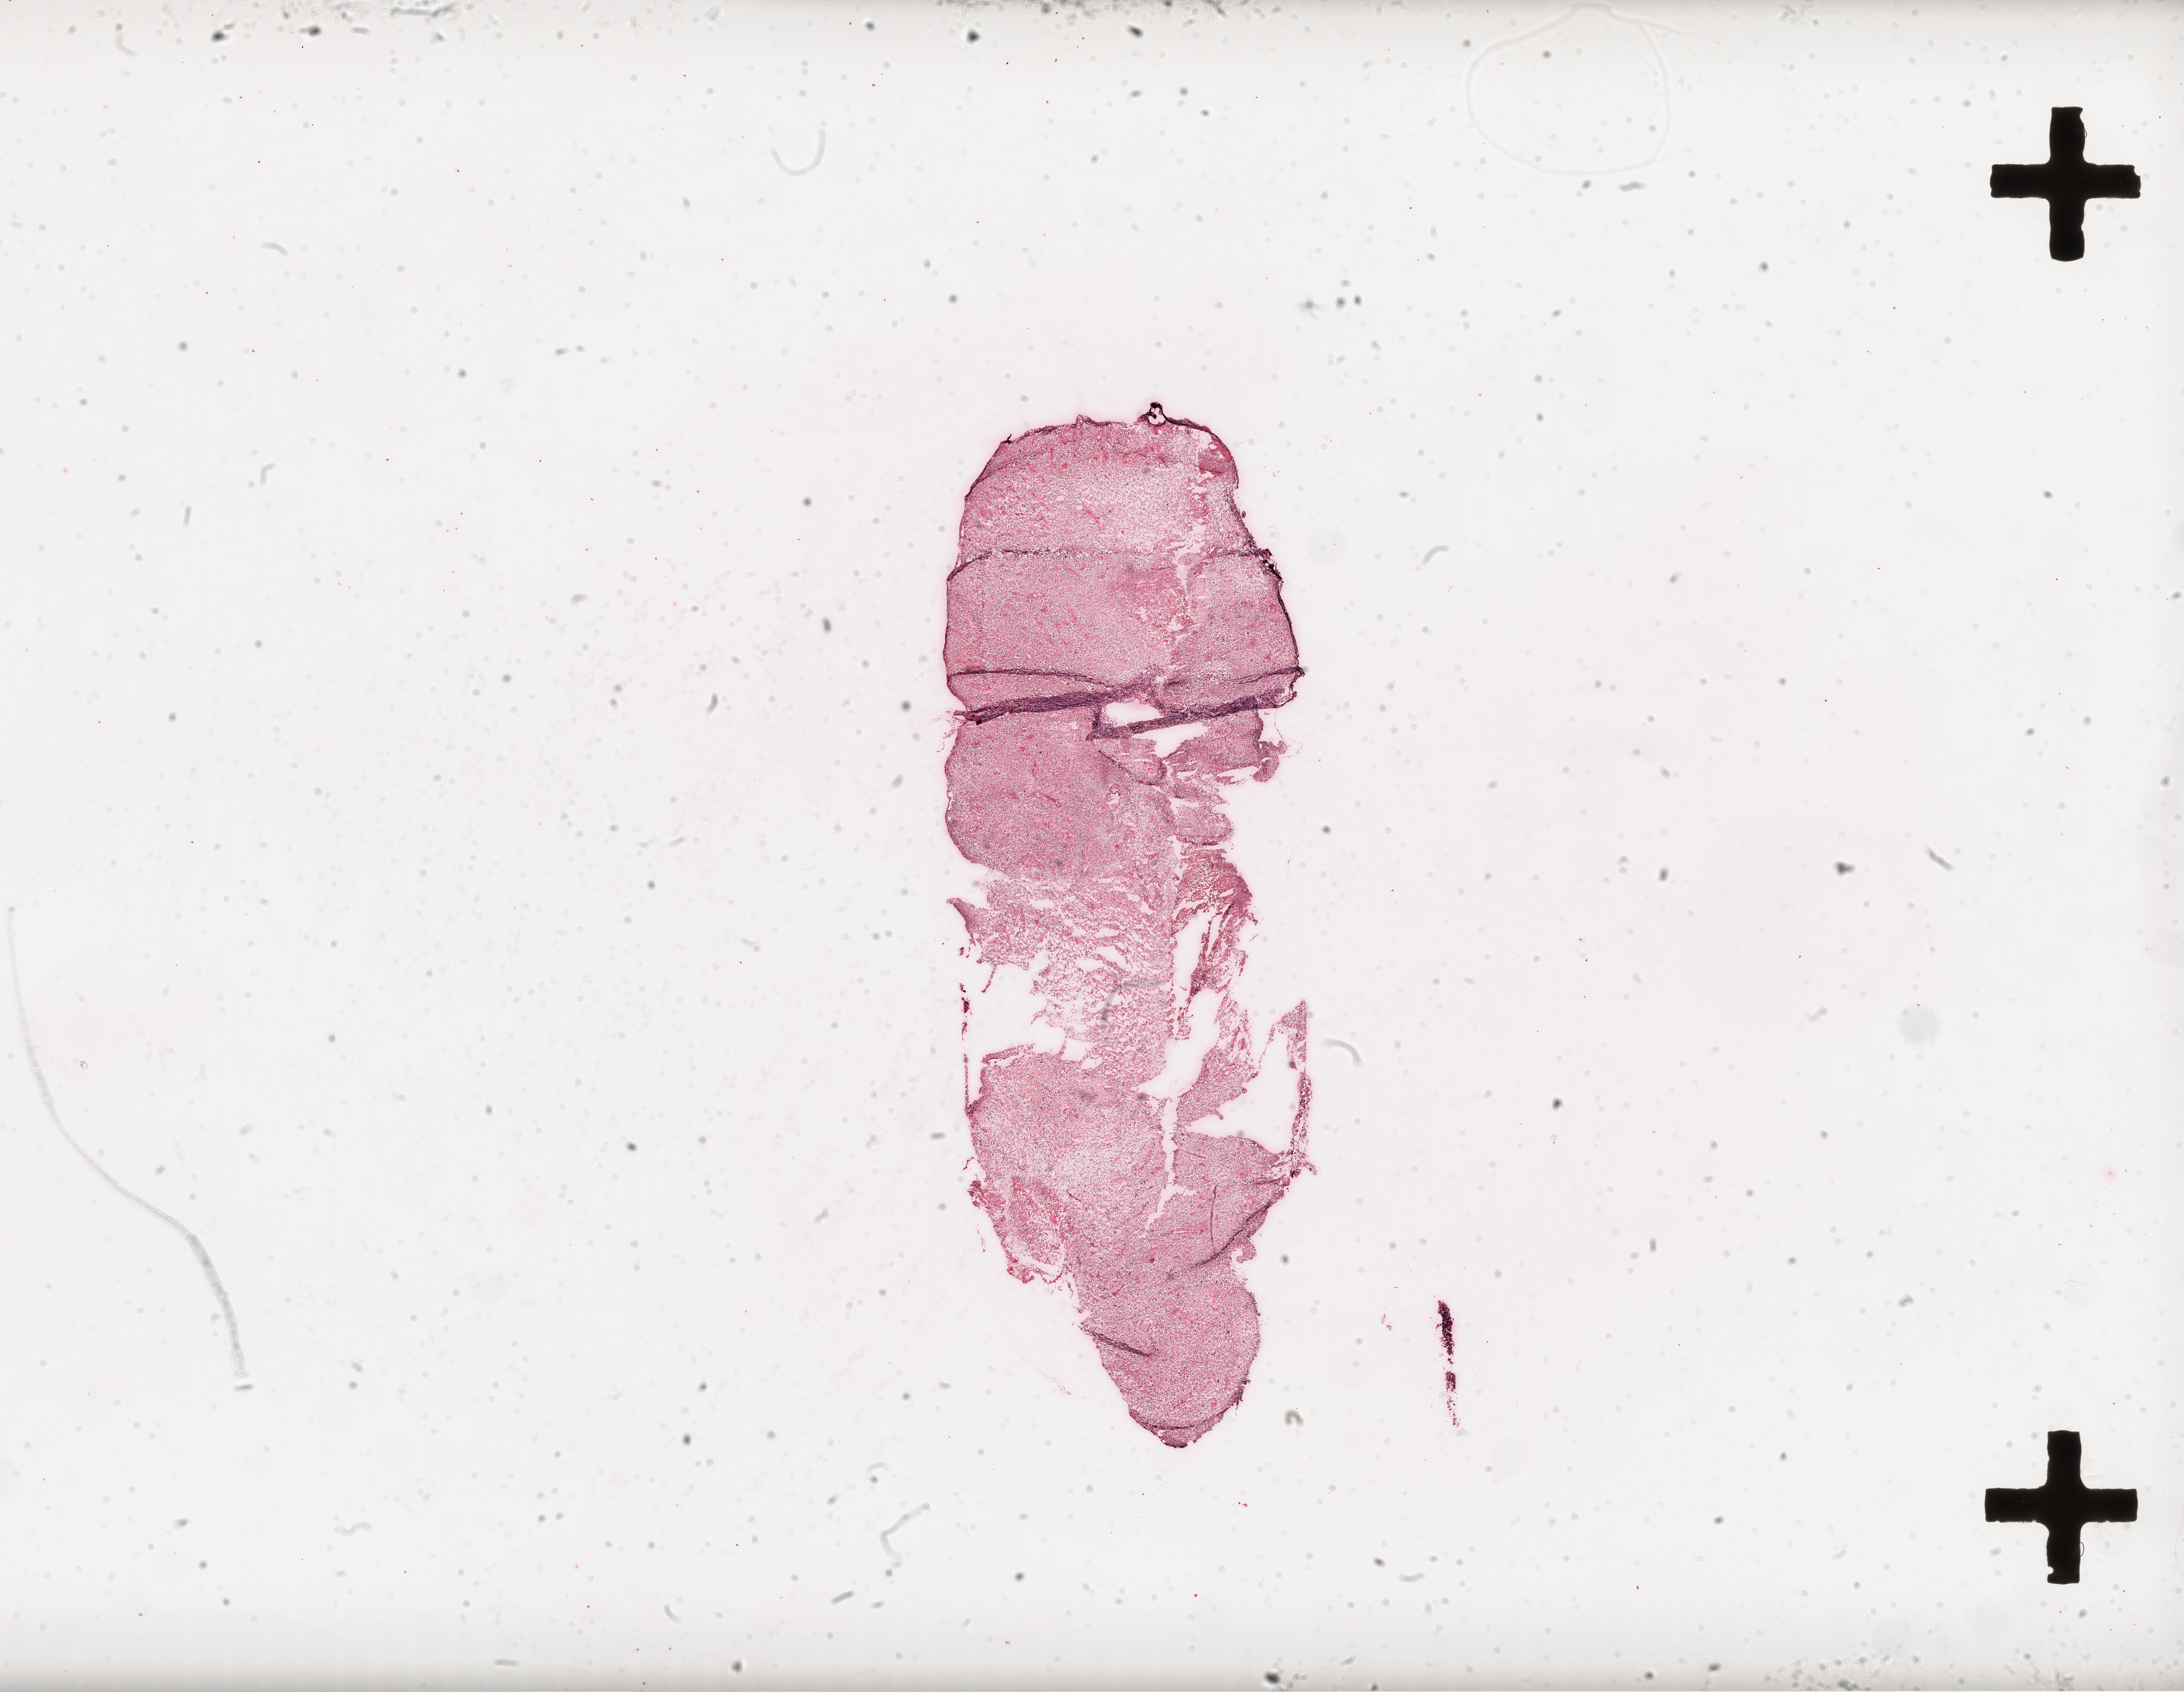
Digitized H&E tissue section (whole slide) — a low-resolution overview of the entire scanned area, about 28.5 x 22.1 mm, frozen section, primary tumour sample from the brain. Patient: female, age at initial diagnosis 60 years. Composition of this section per pathologist review: tumour cells 95%, tumour nuclei 100%, normal cells 0%, stromal cells 0%, necrosis 5%.
• histologic diagnosis: Glioblastoma